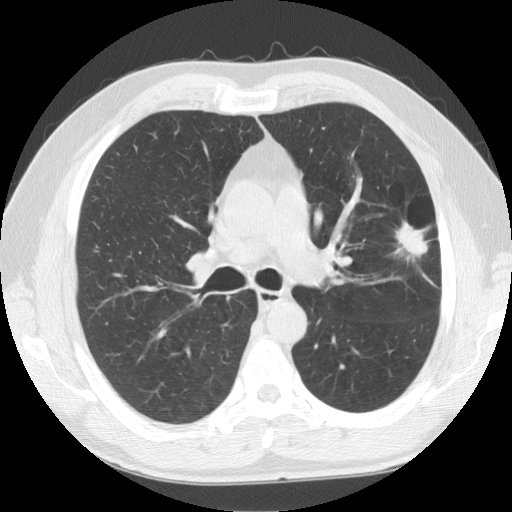
Low-dose screening chest CT, one axial slice; slice 92 of 141 in the series (ordered by position); 120 kVp; lung window (W 1500 / L -600 HU); 2.5 mm slice thickness; 512 × 512 image matrix, field of view 360 × 360 mm.
Structures marked on this image (manually delineated by an expert):
- lesion 1 (tumor, upper lobe of left lung): box from (x=394, y=222) to (x=429, y=262) px